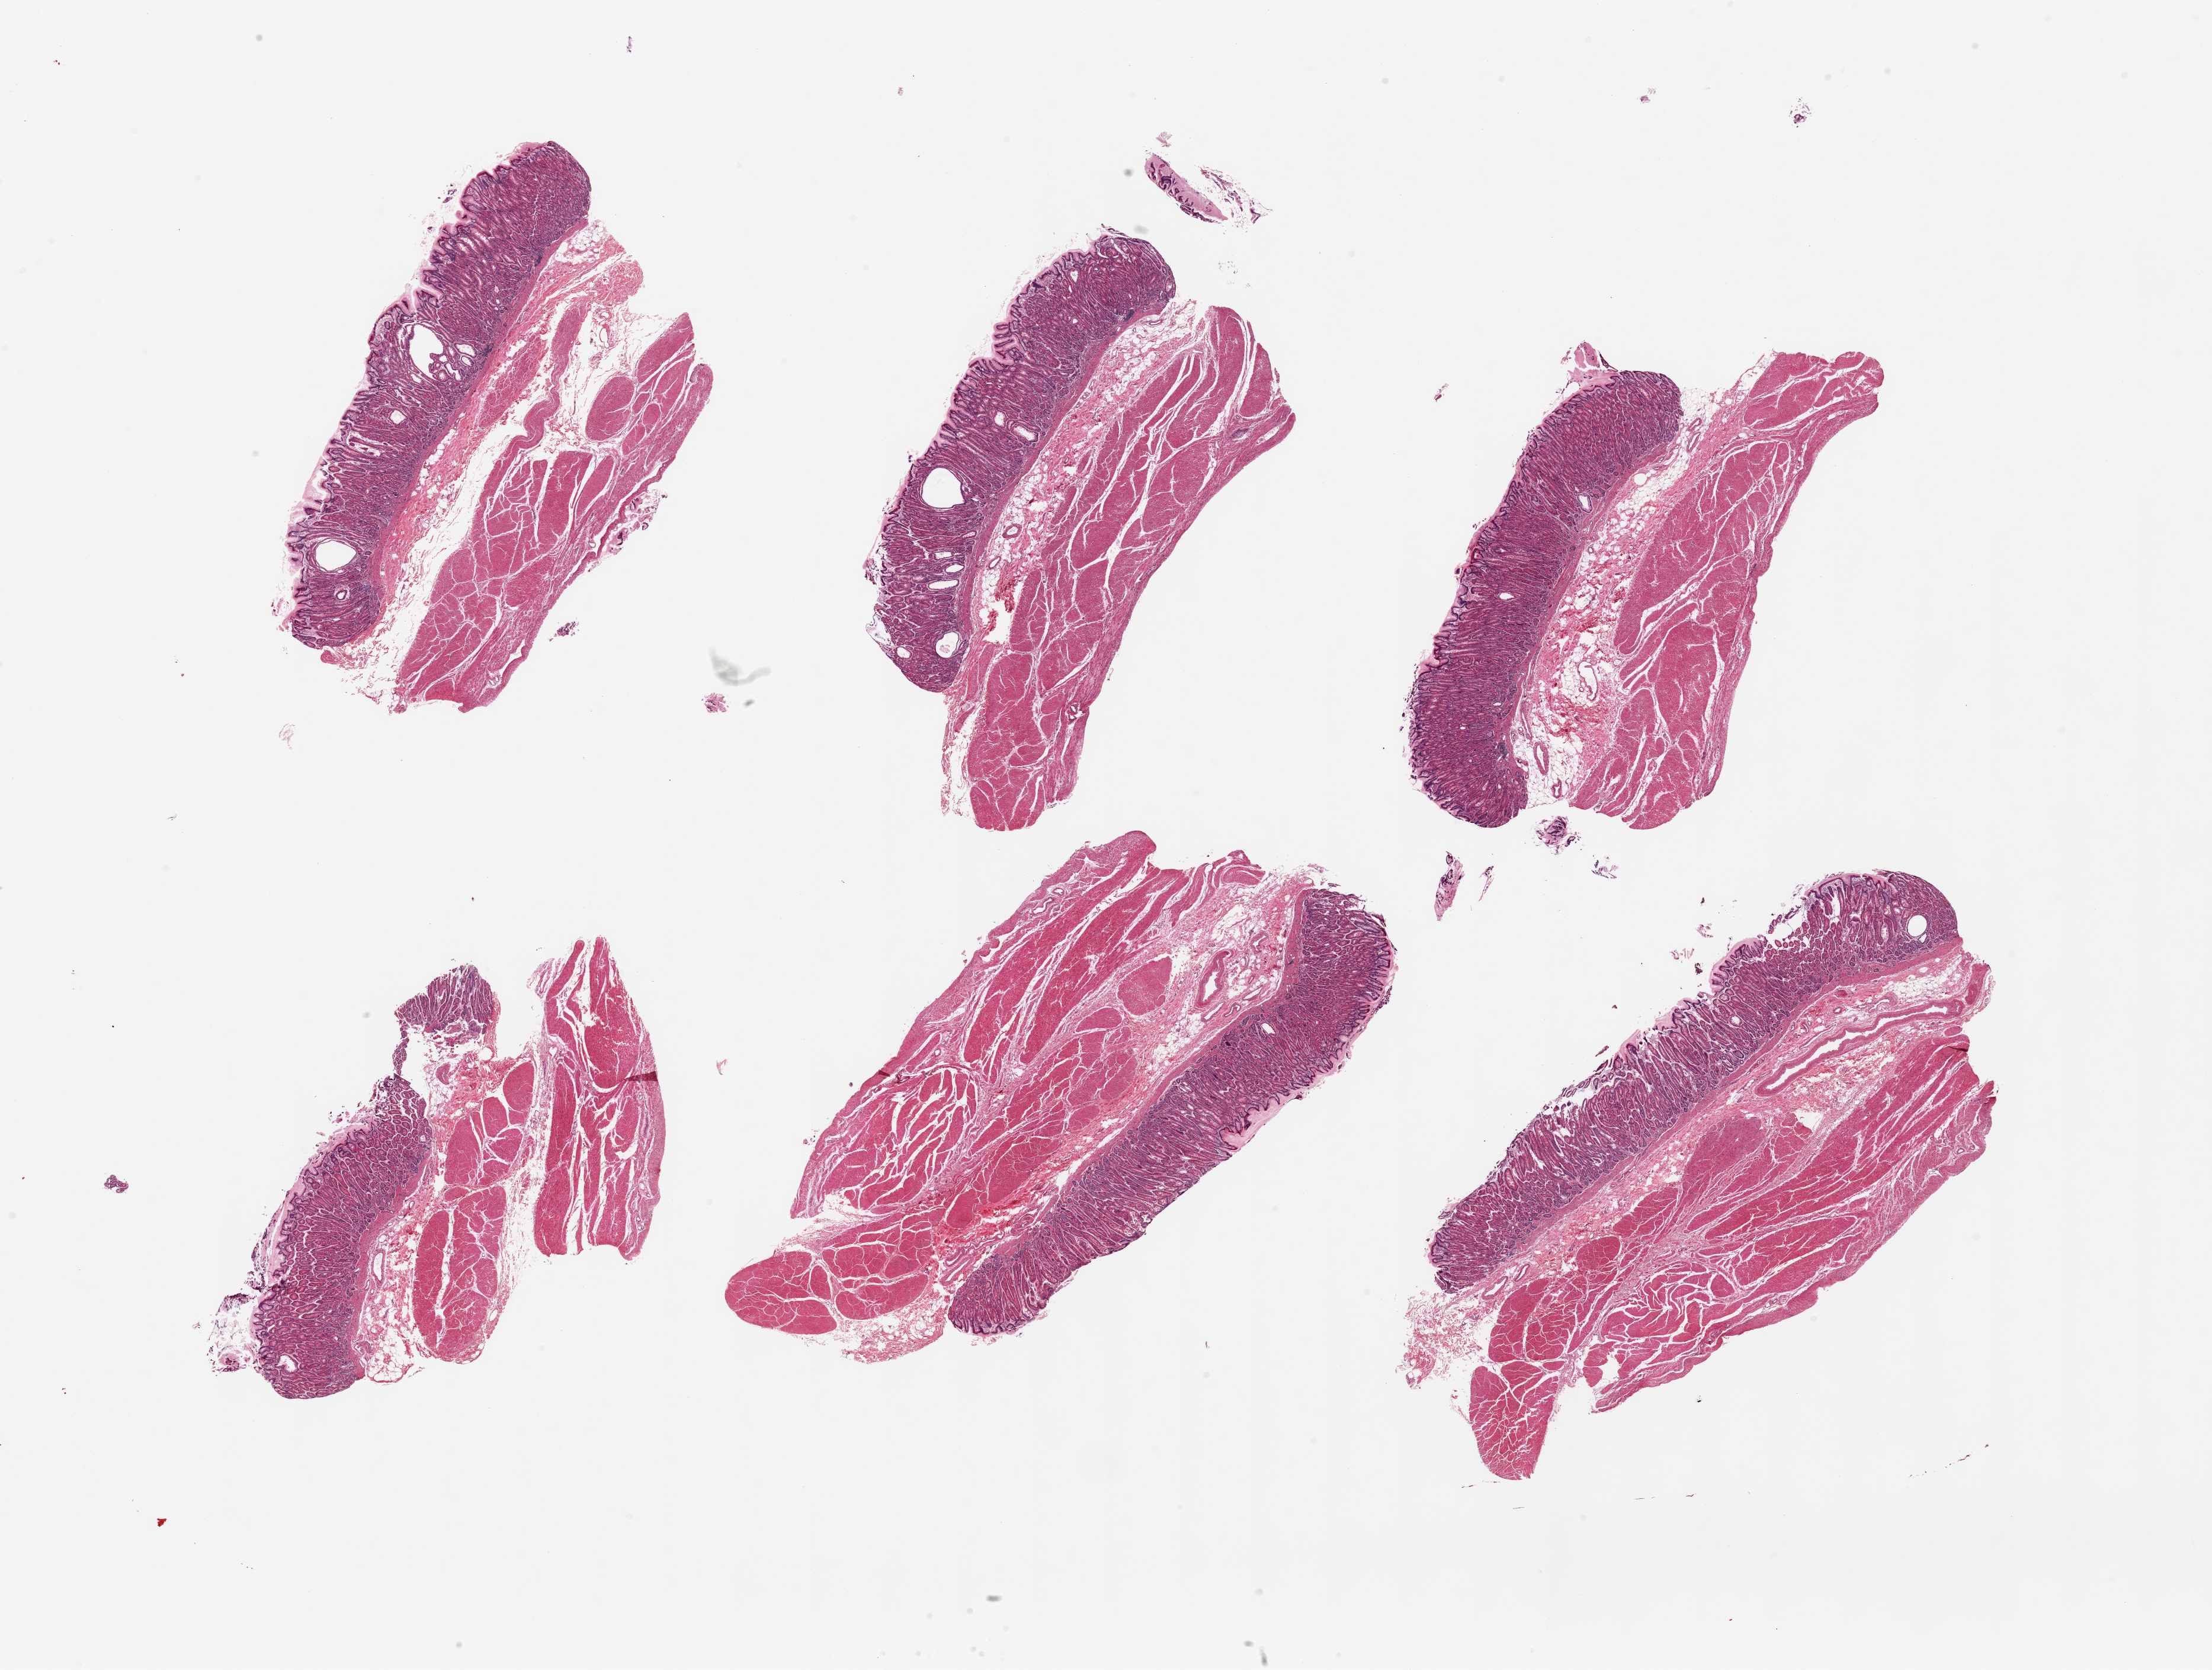
Digitized hematoxylin and eosin (H&E)-stained section, brightfield, low-resolution overview of the scanned area, about 29.5 x 22.3 mm. PAXgene-fixed, paraffin-embedded tissue. Section of stomach (target tissue). Donor tissue sample. Donor: female.
Pathologist's review note for this sample: 6 pieces, mucosa up to ~1.3 mm, ~30-40% thickness, focal microcystic metaplastic changes.